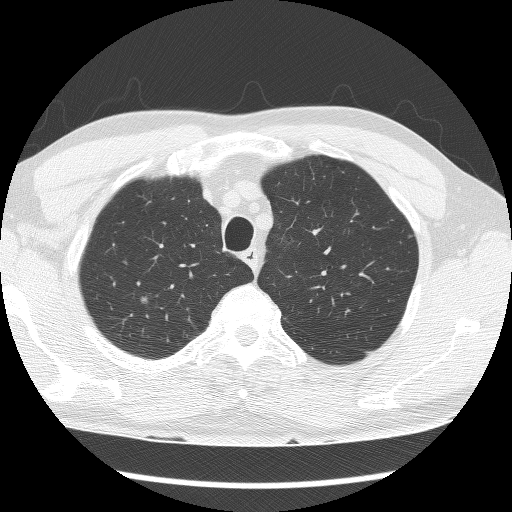
Axial slice from a low-dose chest CT screening exam. Baseline annual screen. Lung window (W 1500 / L -600 HU). 2.5 mm slice thickness. Lung (sharp) reconstruction kernel (BONE). 512 × 512 image matrix, field of view 340 × 340 mm. Male, age 66 years at enrolment. Current smoker at enrolment.
Expert reader's lesion annotation, bounding box <126,286,160,314> (left, top, right, bottom; pixels). The screening reader recorded 2 non-calcified nodules or masses ≥4 mm on this exam (right upper lobe, right upper lobe); which of them this box marks is not recorded. Official screen result: positive, change unspecified: nodule(s) >= 4 mm or enlarging nodule(s), mass(es), or other non-specific abnormalities suspicious for lung cancer. Participant outcome: lung cancer diagnosed 596 days after this screen (after the second annual screen) — squamous cell carcinoma, NOS, right upper lobe, moderately differentiated (G2), stage IIB (AJCC 6th edition), 39 mm at pathology.